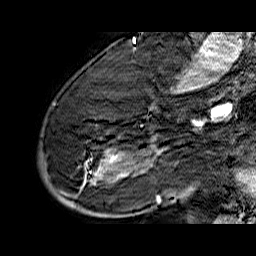
Breast MRI (dynamic contrast-enhanced), one sagittal slice; dynamic contrast-enhanced series, time point 2 of 6 at this slice position (early post-contrast); 1.5 T; TE 6.5 ms, TR 32.9 ms; 4 mm slice thickness; 256 × 256 image matrix. Female patient. From the clinical record (not read from this slice): setting: breast cancer imaged before/during neoadjuvant chemotherapy; receptor status: HR-positive, HER2-negative.
Outlined on this slice (semi-automatic segmentation, software-assisted and operator-edited):
- analysis volume of interest (the breast-tissue region the enhancement analysis was run in; not a lesion): bounding box [x1, y1, x2, y2] px = [39, 74, 176, 210]
- tumour enhancement mask (voxels above the 100 % enhancement threshold inside the analysis volume of interest): [52, 105, 163, 203]